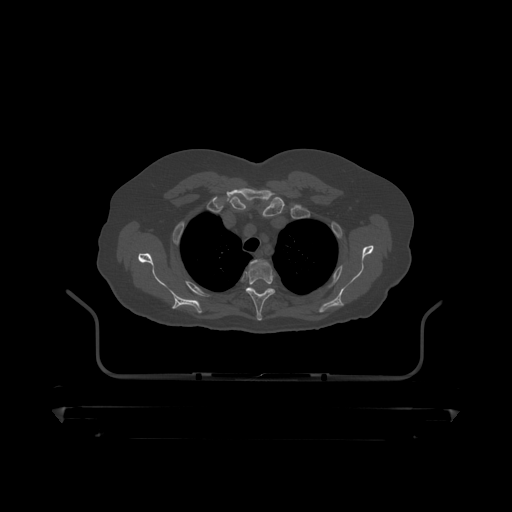
CT including the spine, one axial slice. Position 356 of 390 along the scan axis. 120 kVp. Bone window (W 1800 / L 400 HU). 1.25 mm slice thickness. 512 × 512 image matrix, field of view 650 × 650 mm. Patient: male, 60 years. Case-level facts recorded for this patient, not image findings: primary cancer: prostate.
Annotated regions visible in this slice (semi-automatically segmented with operator editing):
- T2 vertebra: box from (x=251, y=260) to (x=261, y=265) px
- T3 vertebra: (x=246, y=260)–(x=275, y=319)
- T4 vertebra: (x=248, y=288)–(x=275, y=295)